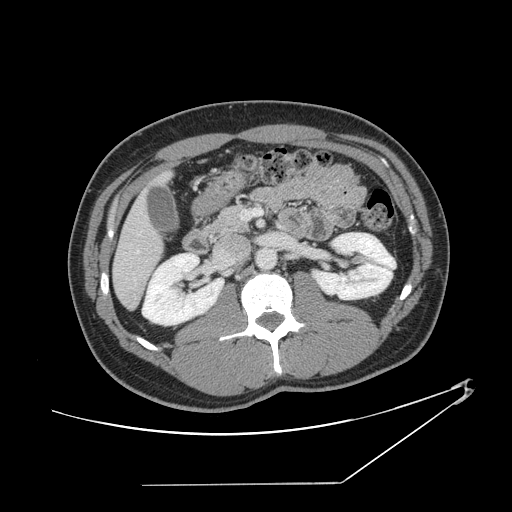
Contrast-enhanced abdominal CT, one axial slice; reconstruction kernel STANDARD; intravenous contrast given; soft-tissue window (W 400 / L 40 HU); 2.5 mm slice thickness; 512 × 512 image matrix. Male patient, age 45 years. Case-level facts recorded for this patient, not image findings: diagnosis: colorectal cancer liver metastases, imaged before liver resection; multiple liver metastases: no; largest metastasis: 1 cm; disease in both lobes: no.
Annotated regions visible in this slice (outlined manually by an expert reader):
- hepatic veins: bounding box [x1, y1, x2, y2] px = [125, 249, 140, 260]
- liver: [114, 198, 163, 308]
- planned liver remnant (the part of the liver to remain after resection): [114, 198, 163, 308]
- portal vein (with intrahepatic branches): [241, 209, 263, 219]